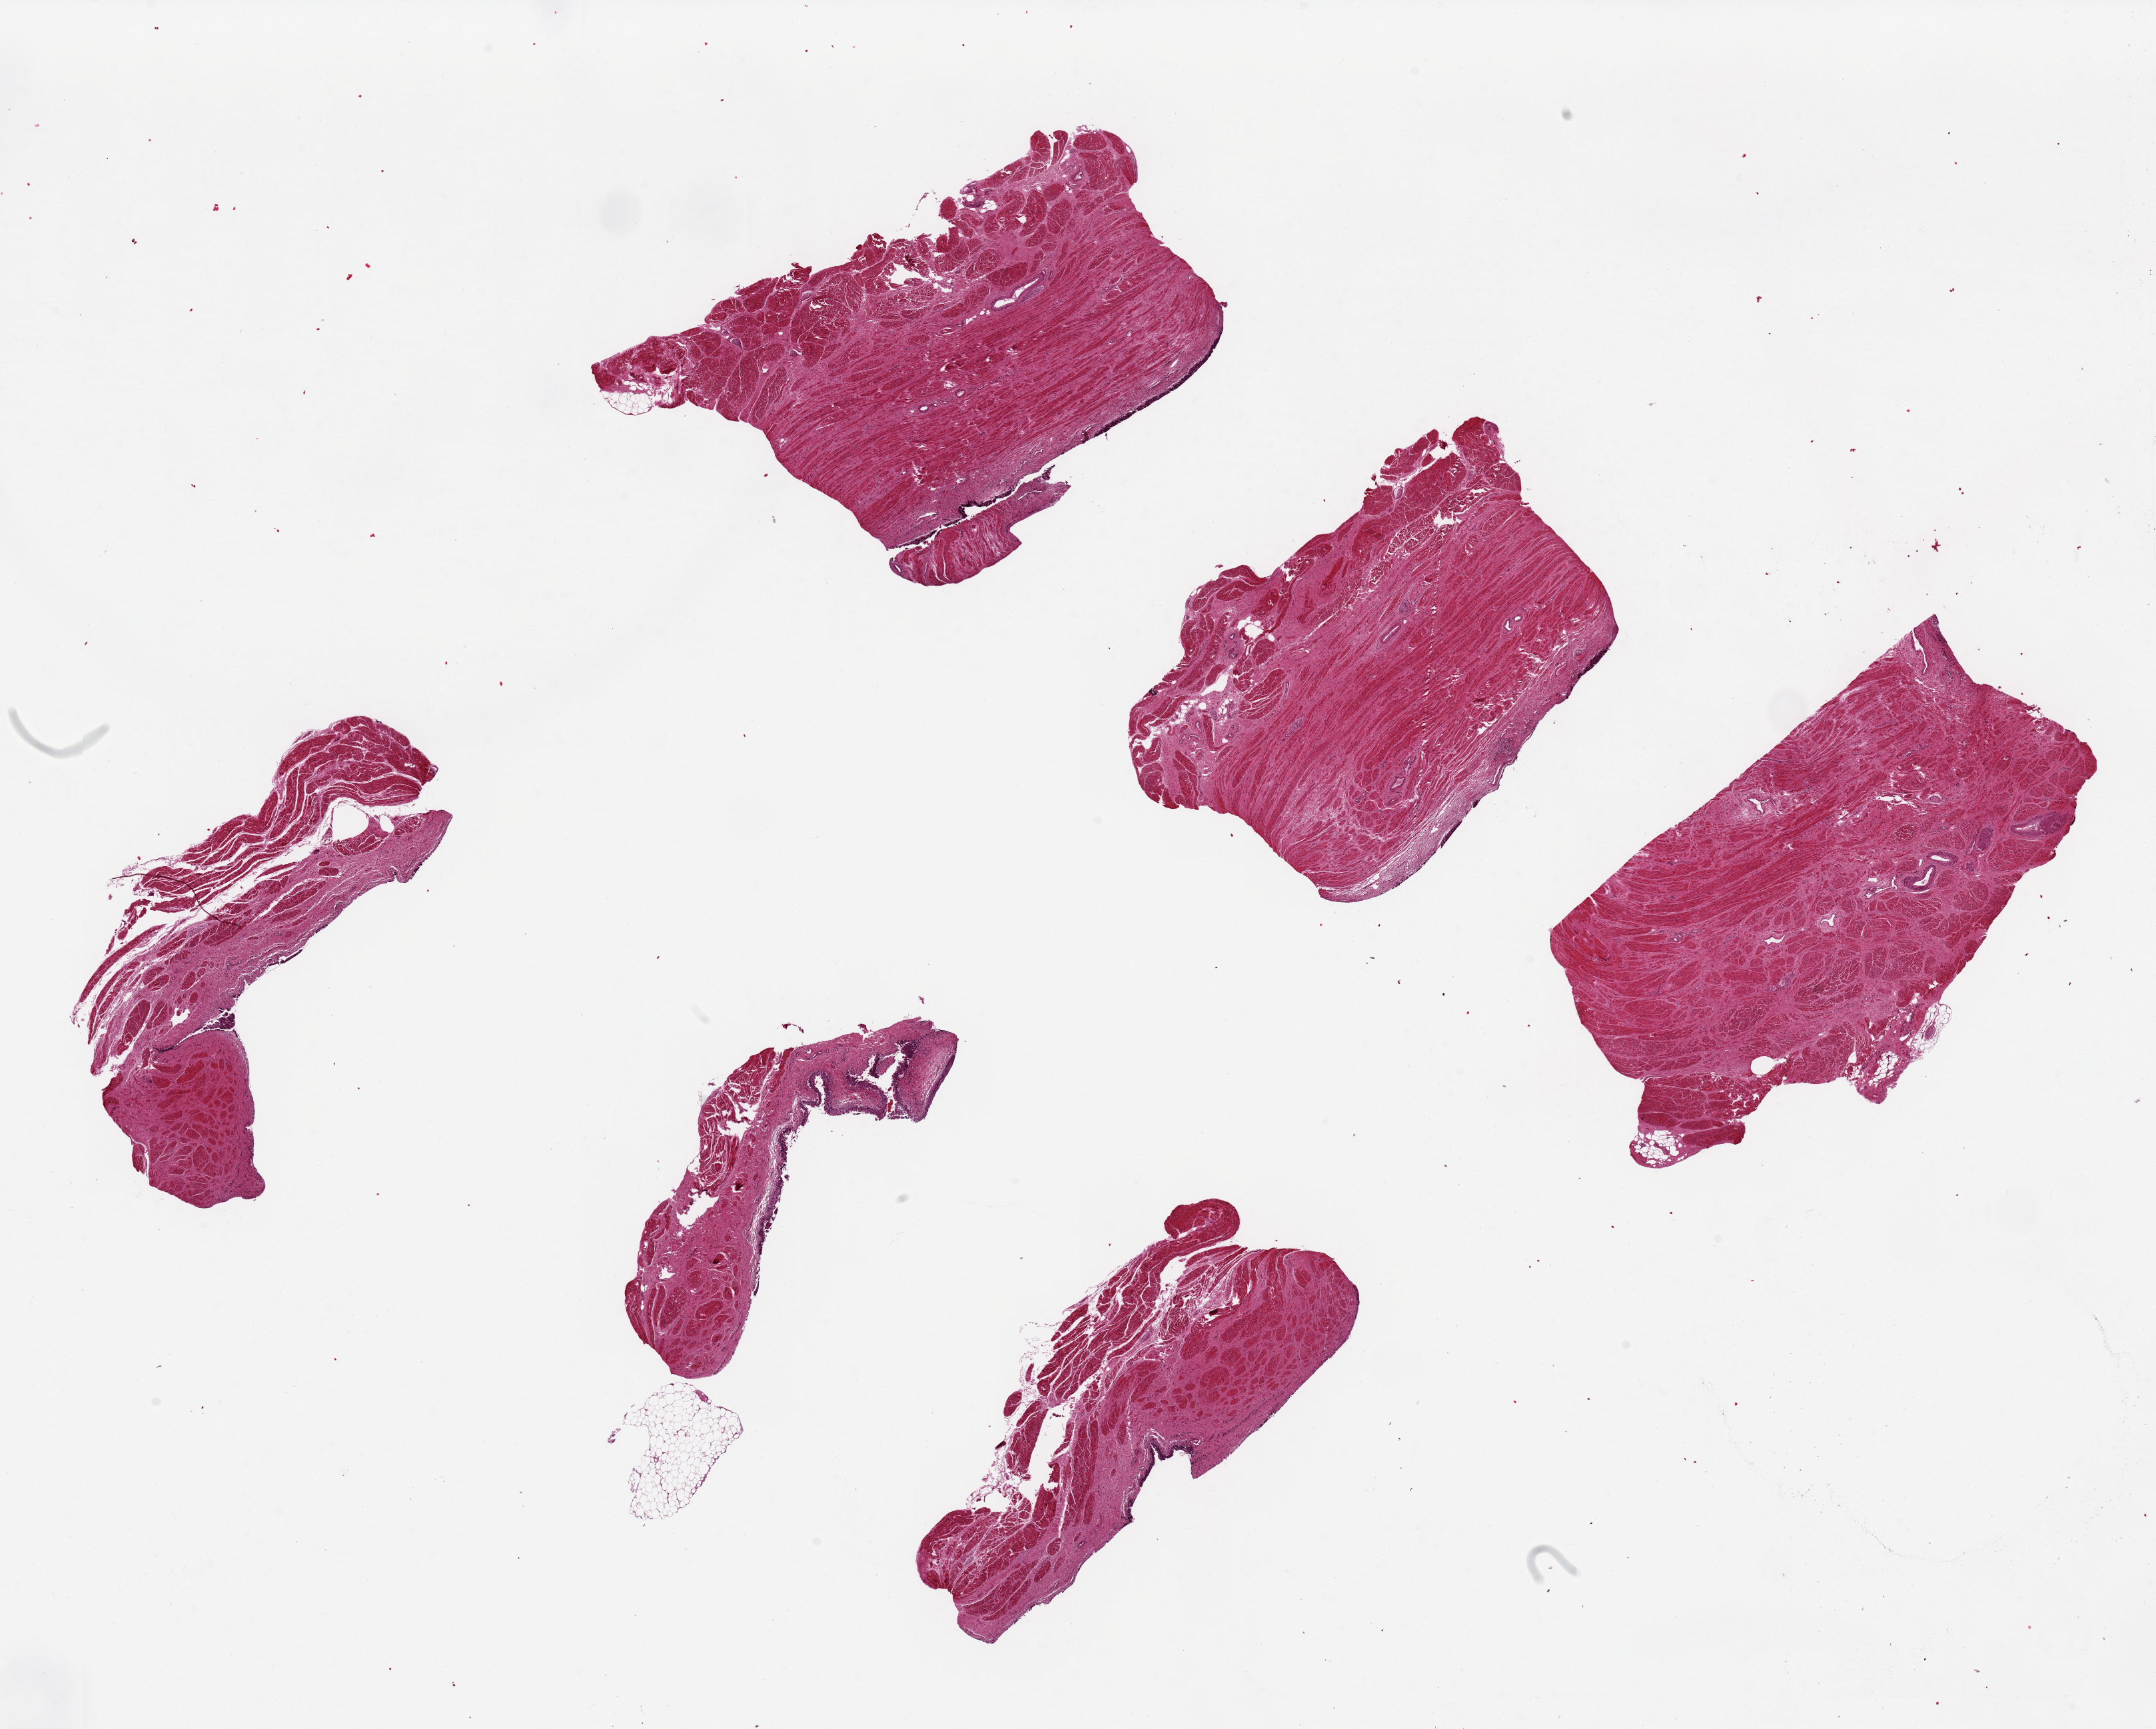
Digitized hematoxylin and eosin (H&E)-stained section, shown as a low-resolution overview of the whole scanned area (about 25.6 x 20.5 mm, from a 20x scan); PAXgene-fixed paraffin-embedded (PFPE) section; target tissue: urinary bladder; tissue donor sample. Donor: male.
Reviewer comment on this tissue sample: 6 pieces, urothelium largely sloughed, mainly detrusor muscle.